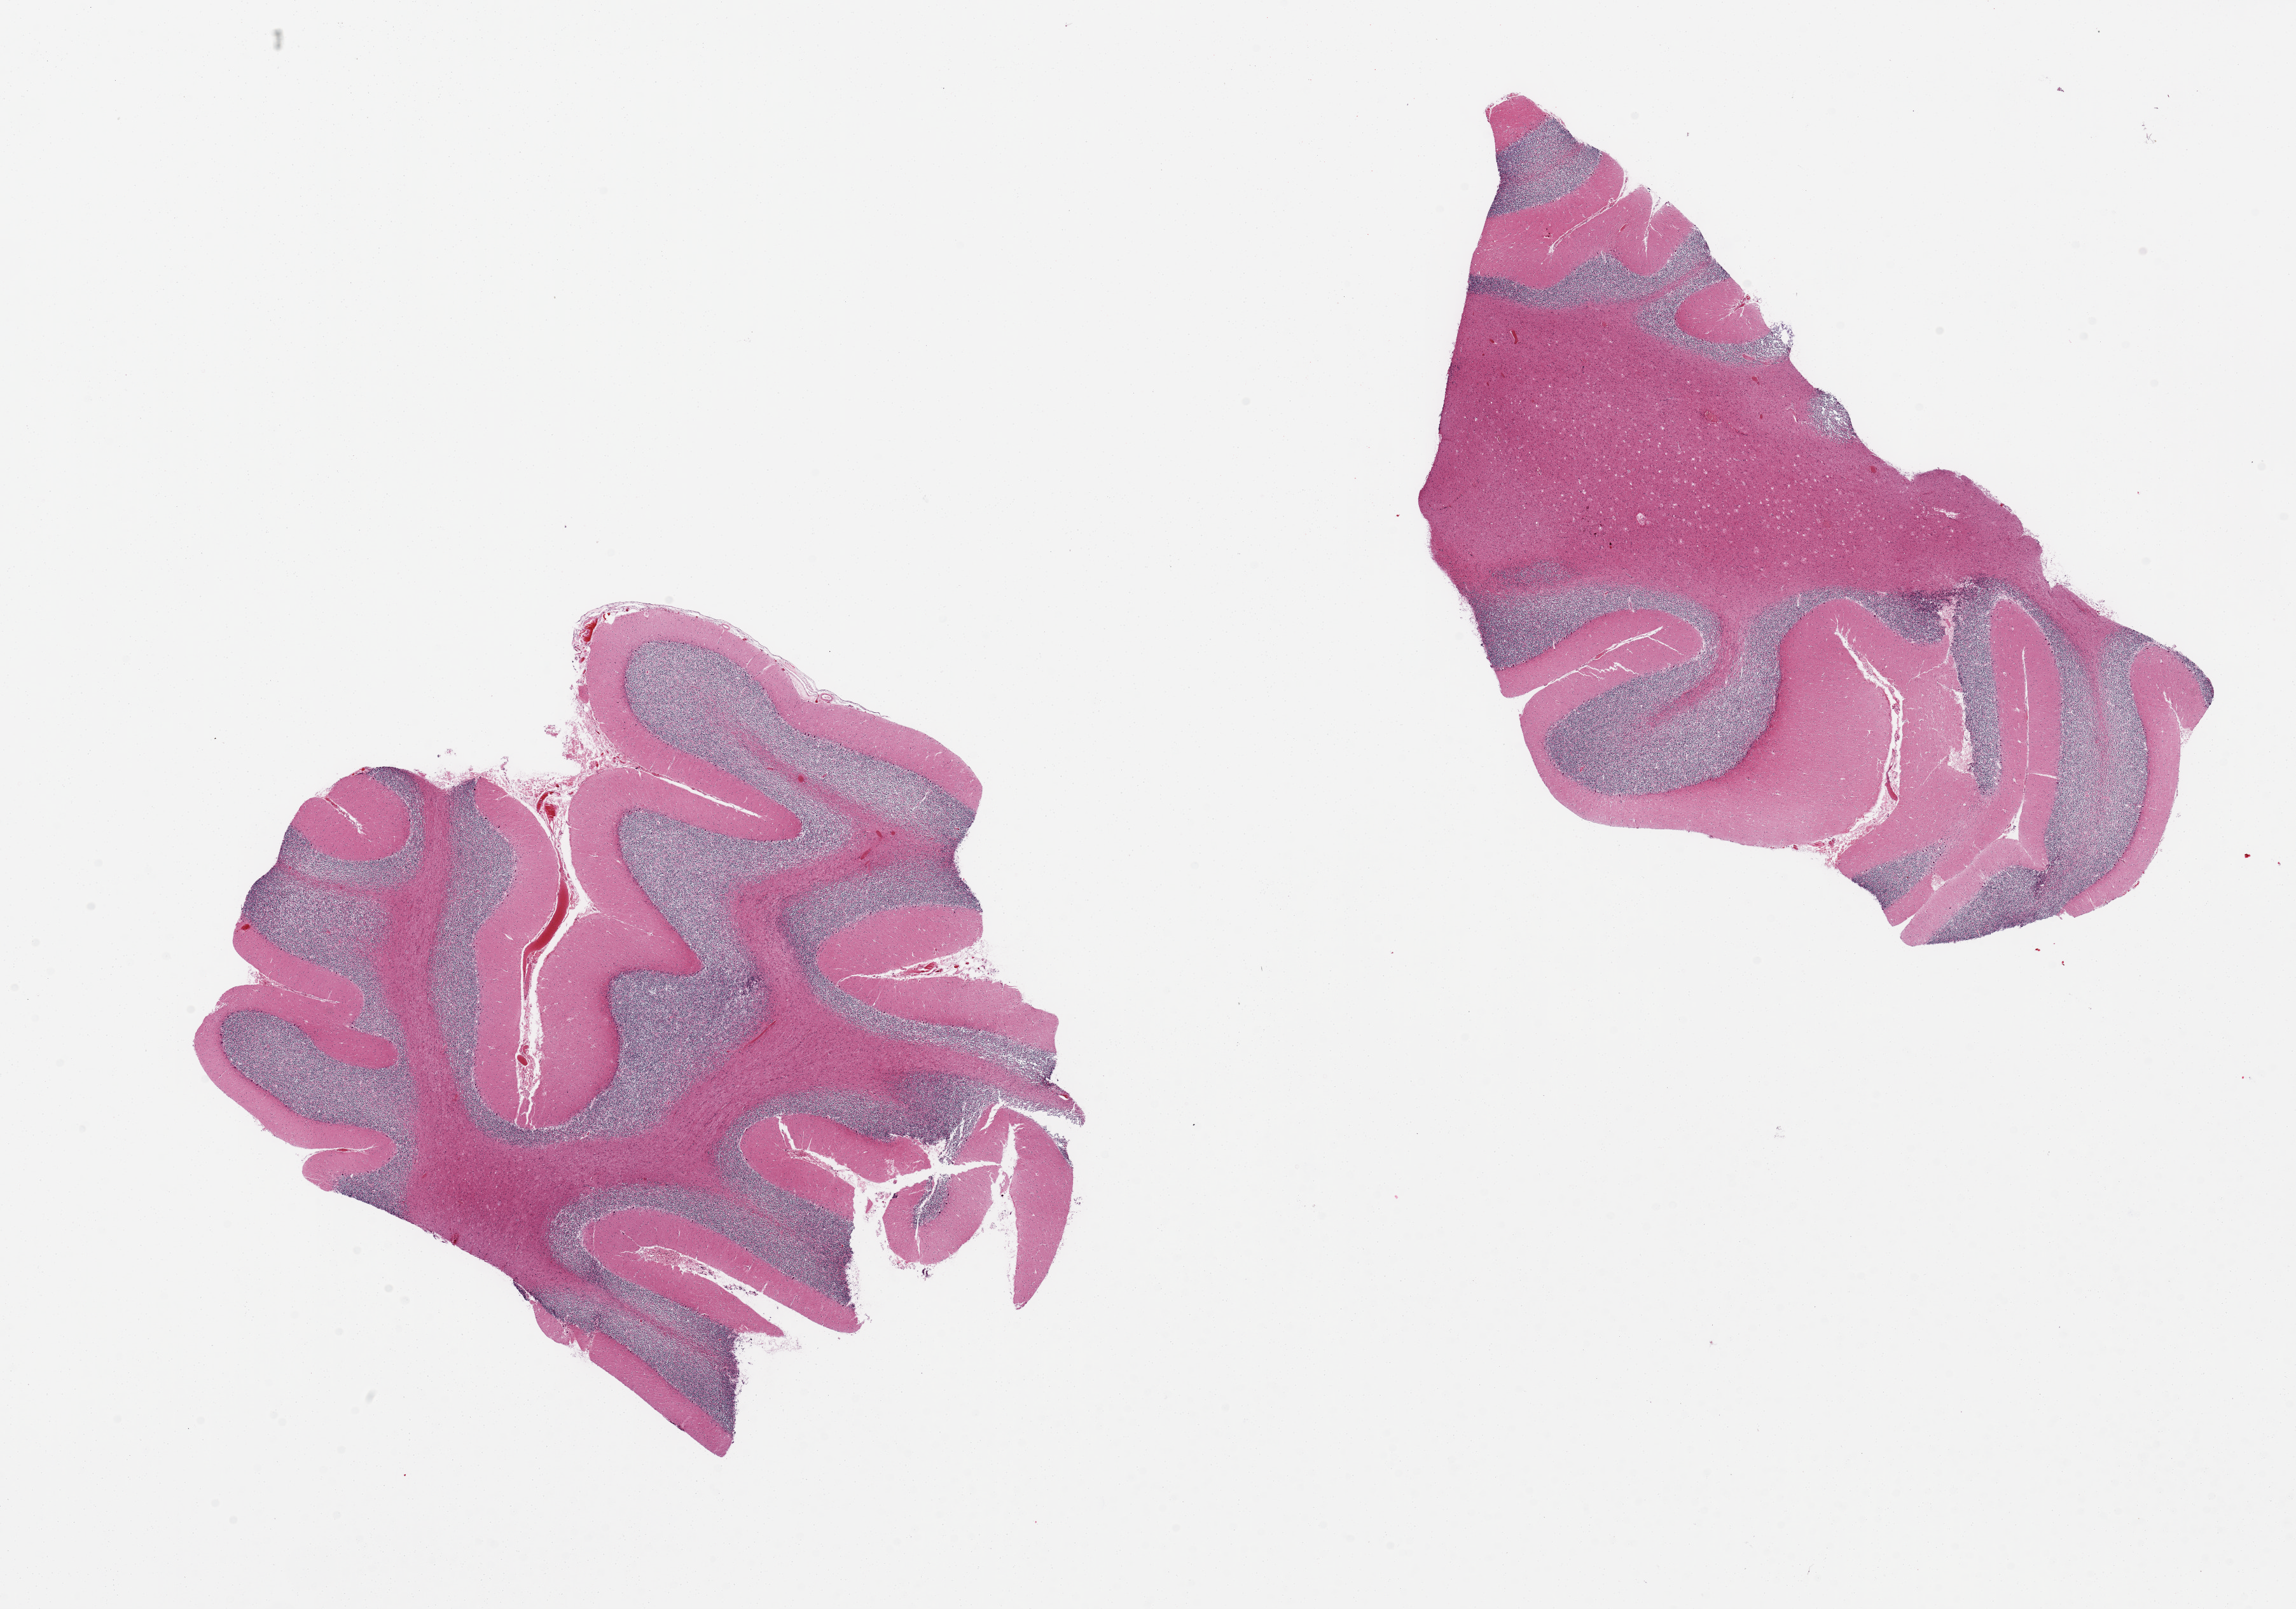
Whole-slide image, haematoxylin and eosin stain — low-resolution overview of the scanned area, about 28.5 x 20.0 mm (slide scanned at 20x). PAXgene-fixed, paraffin-embedded tissue. Section of cerebellum (target tissue). Tissue donor sample. Male donor.
Reviewer comment on this tissue sample: 2 pieces.